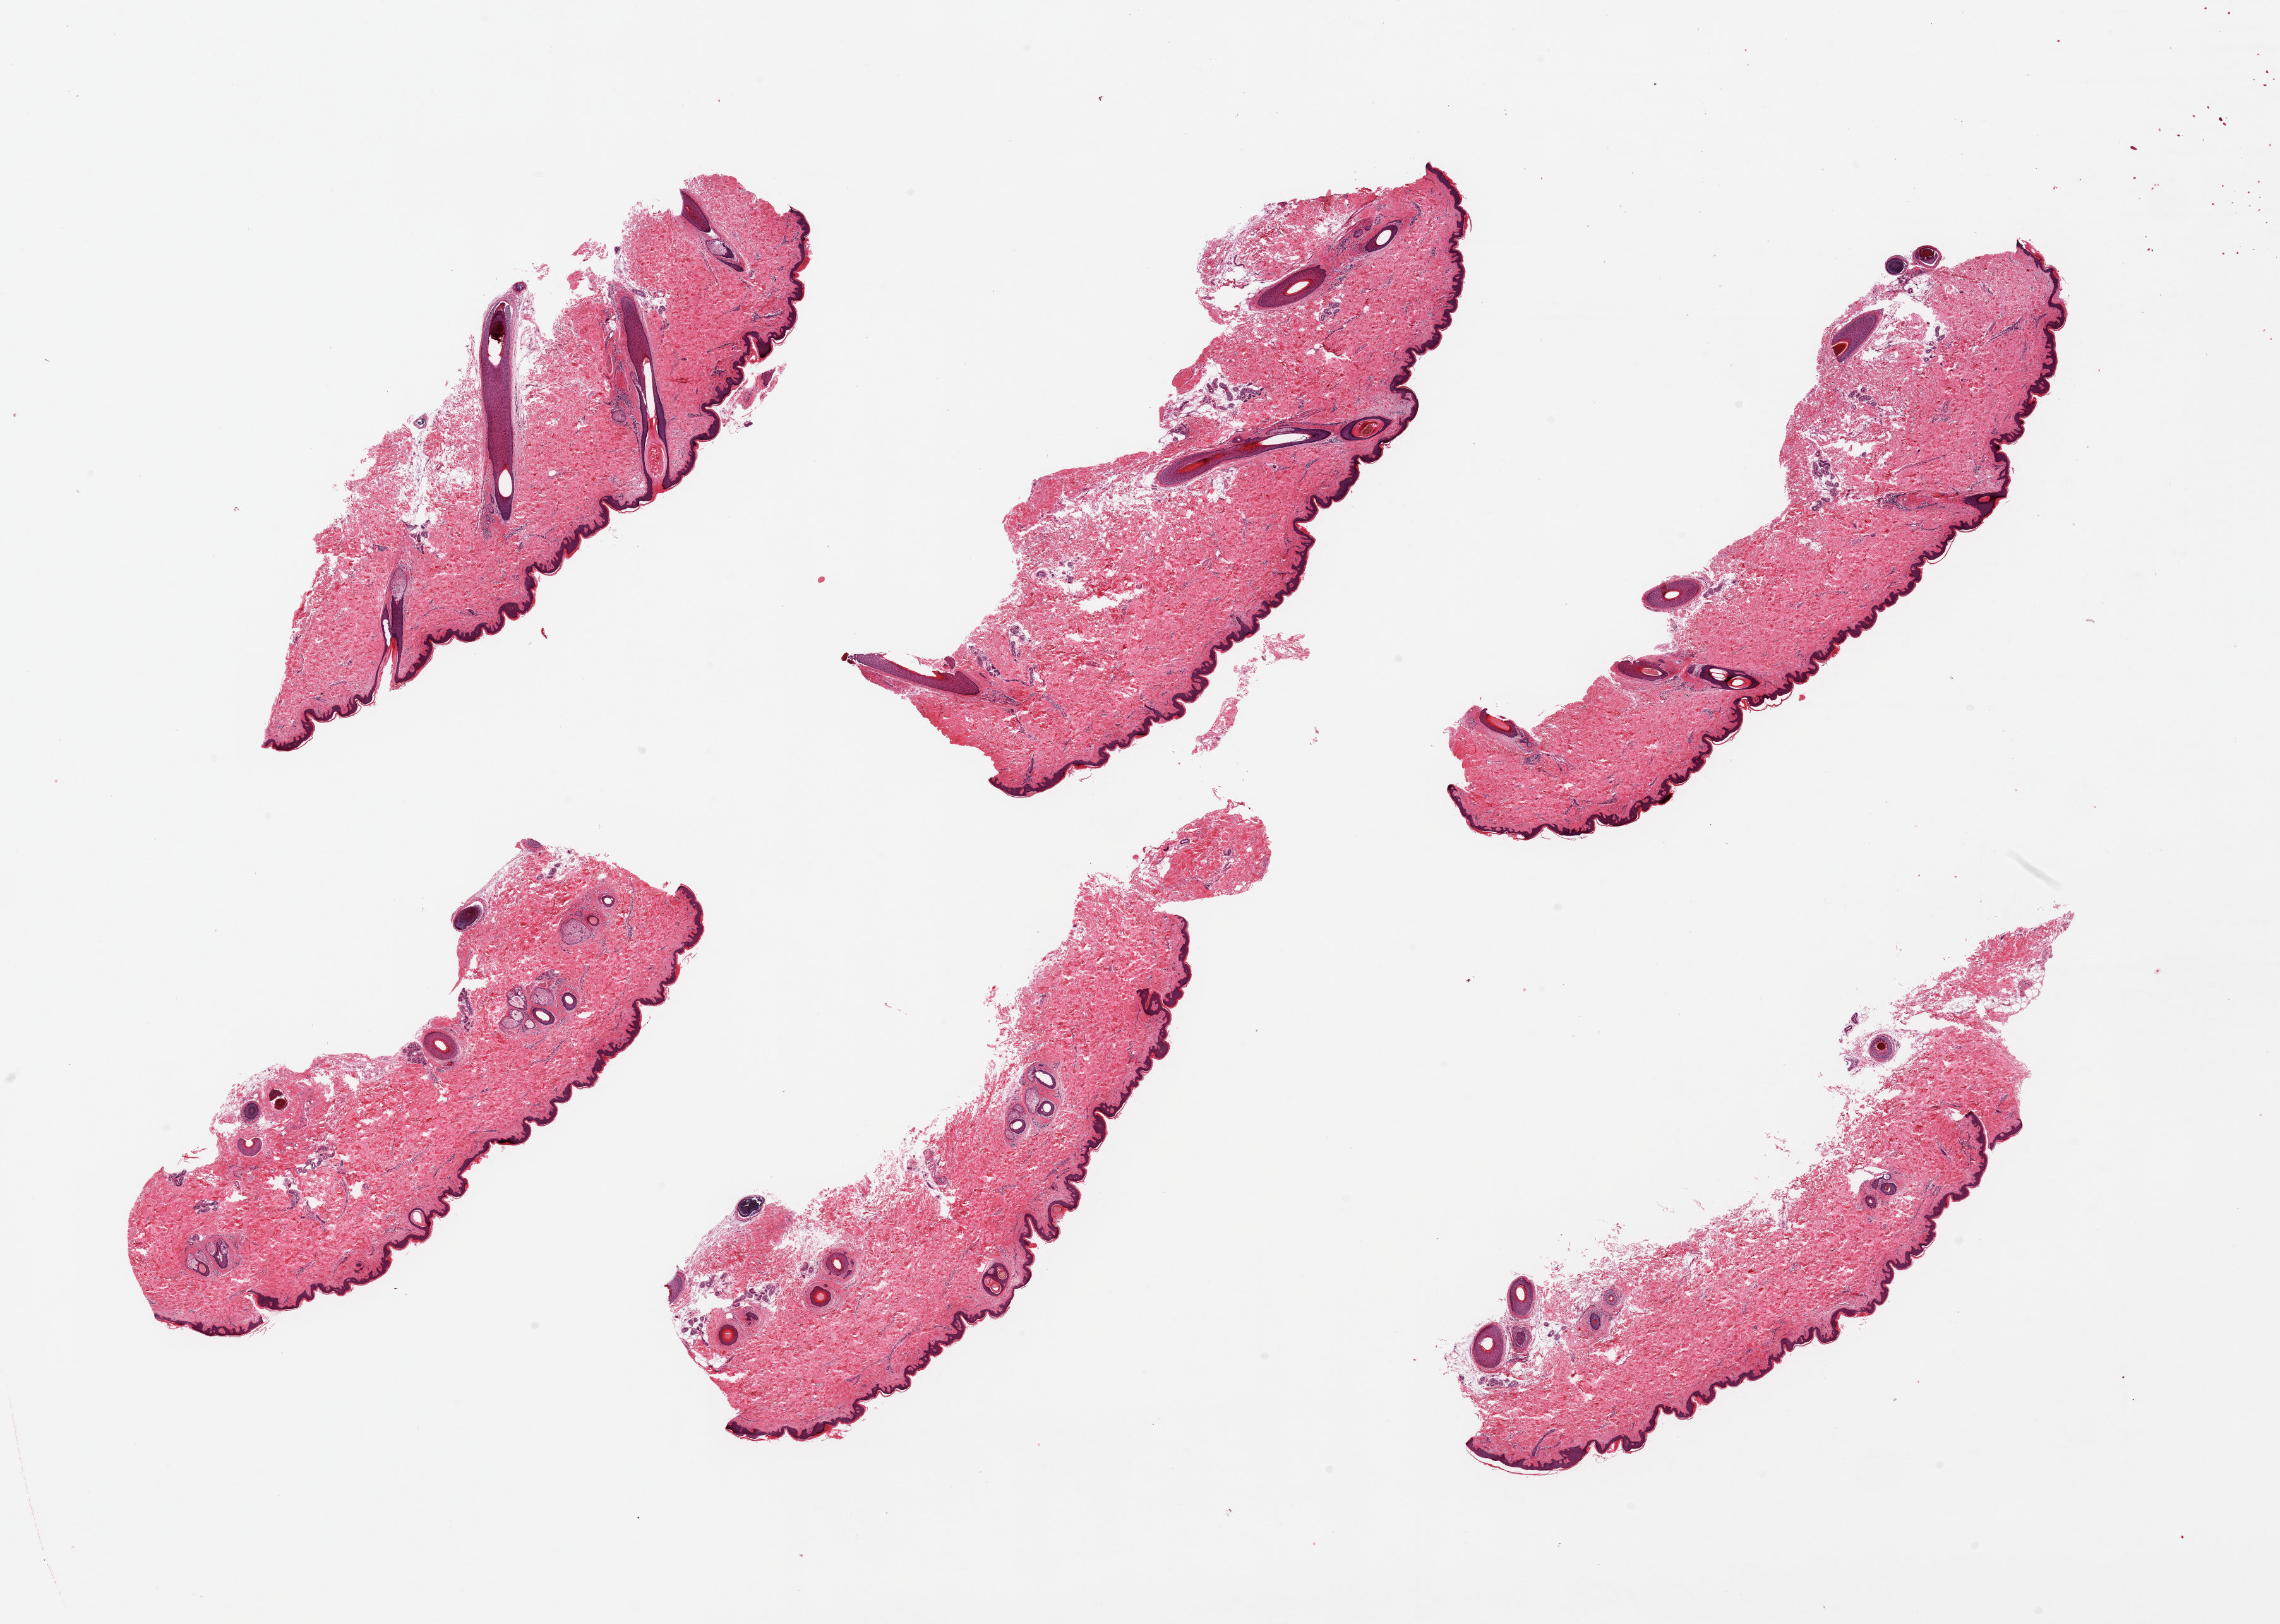
Whole-slide image, hematoxylin and eosin (H&E) stain — whole scanned area (about 28.5 x 20.3 mm, from a 20x scan) shown as a low-resolution overview. PAXgene-fixed, paraffin-embedded tissue. Section of skin of suprapubic region (target tissue). Donor tissue sample. Donor: female.
Review note (as recorded): 6 pieces; well trimmed.